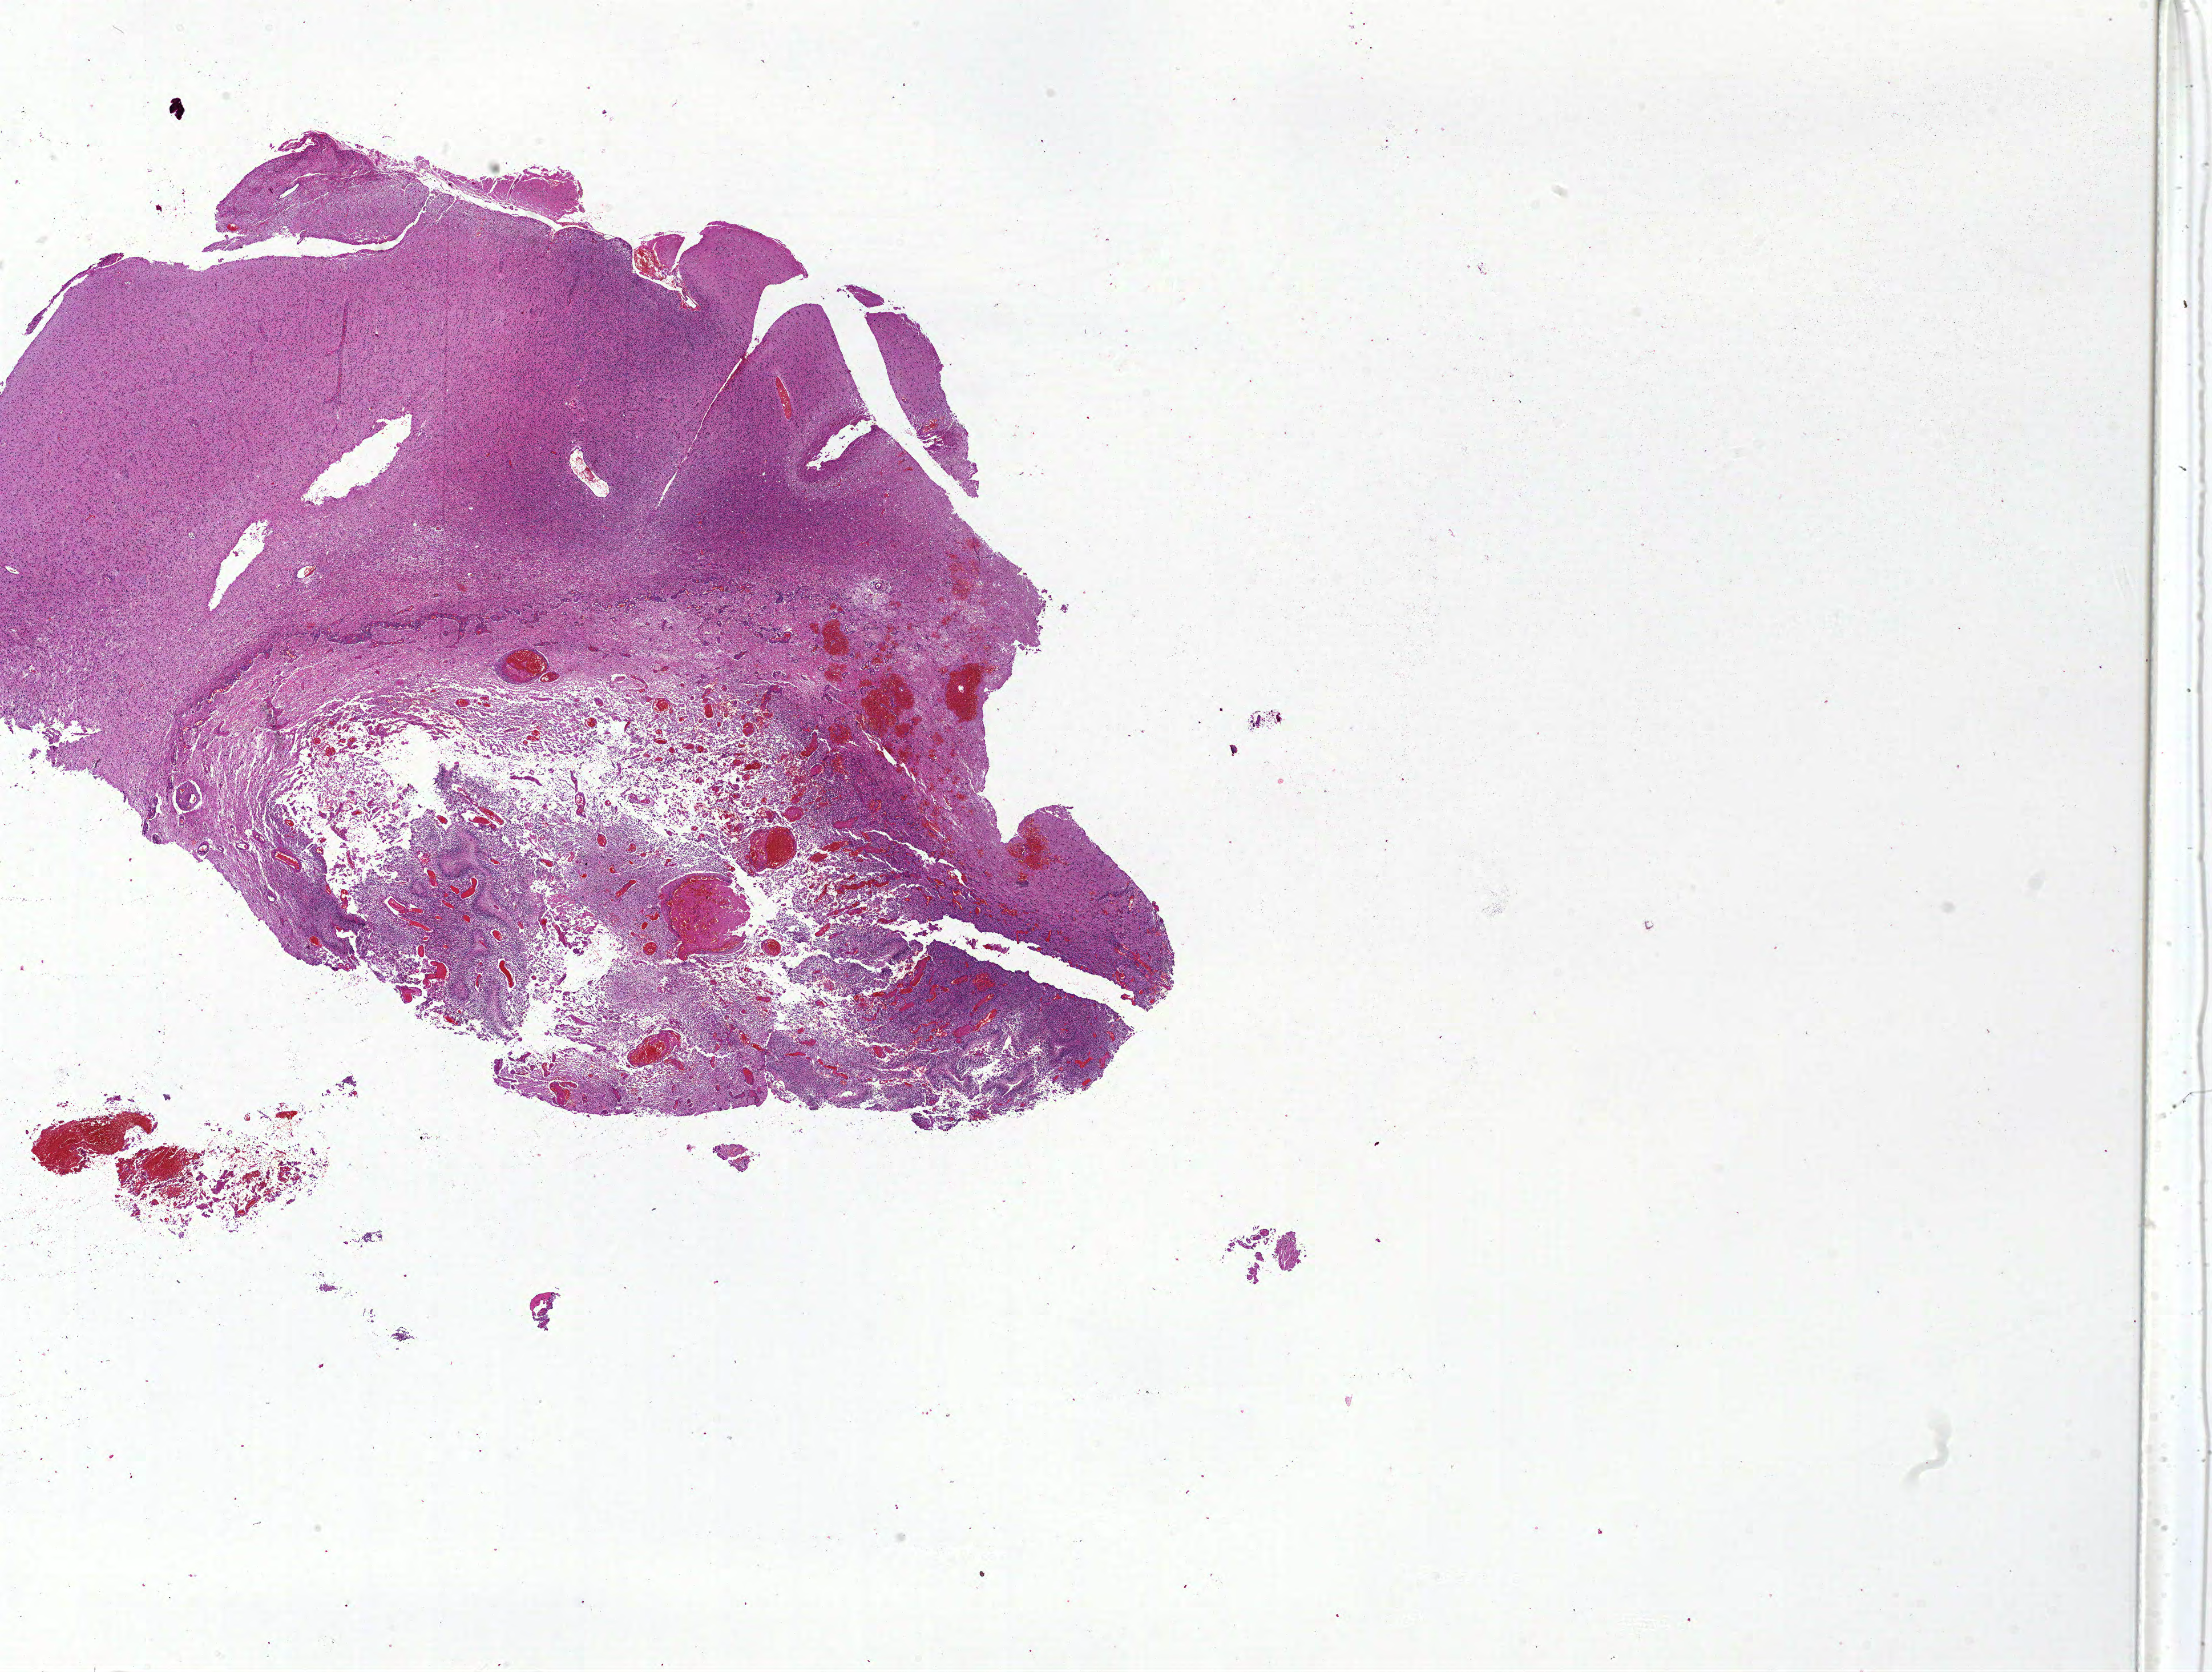
Digitized H&E tissue section (whole slide) — shown as a low-resolution overview of the whole scanned area (about 31.0 x 23.4 mm), FFPE section, primary tumour sample from the brain. Patient: female, age at initial diagnosis 49 years.
* diagnosis: Glioblastoma